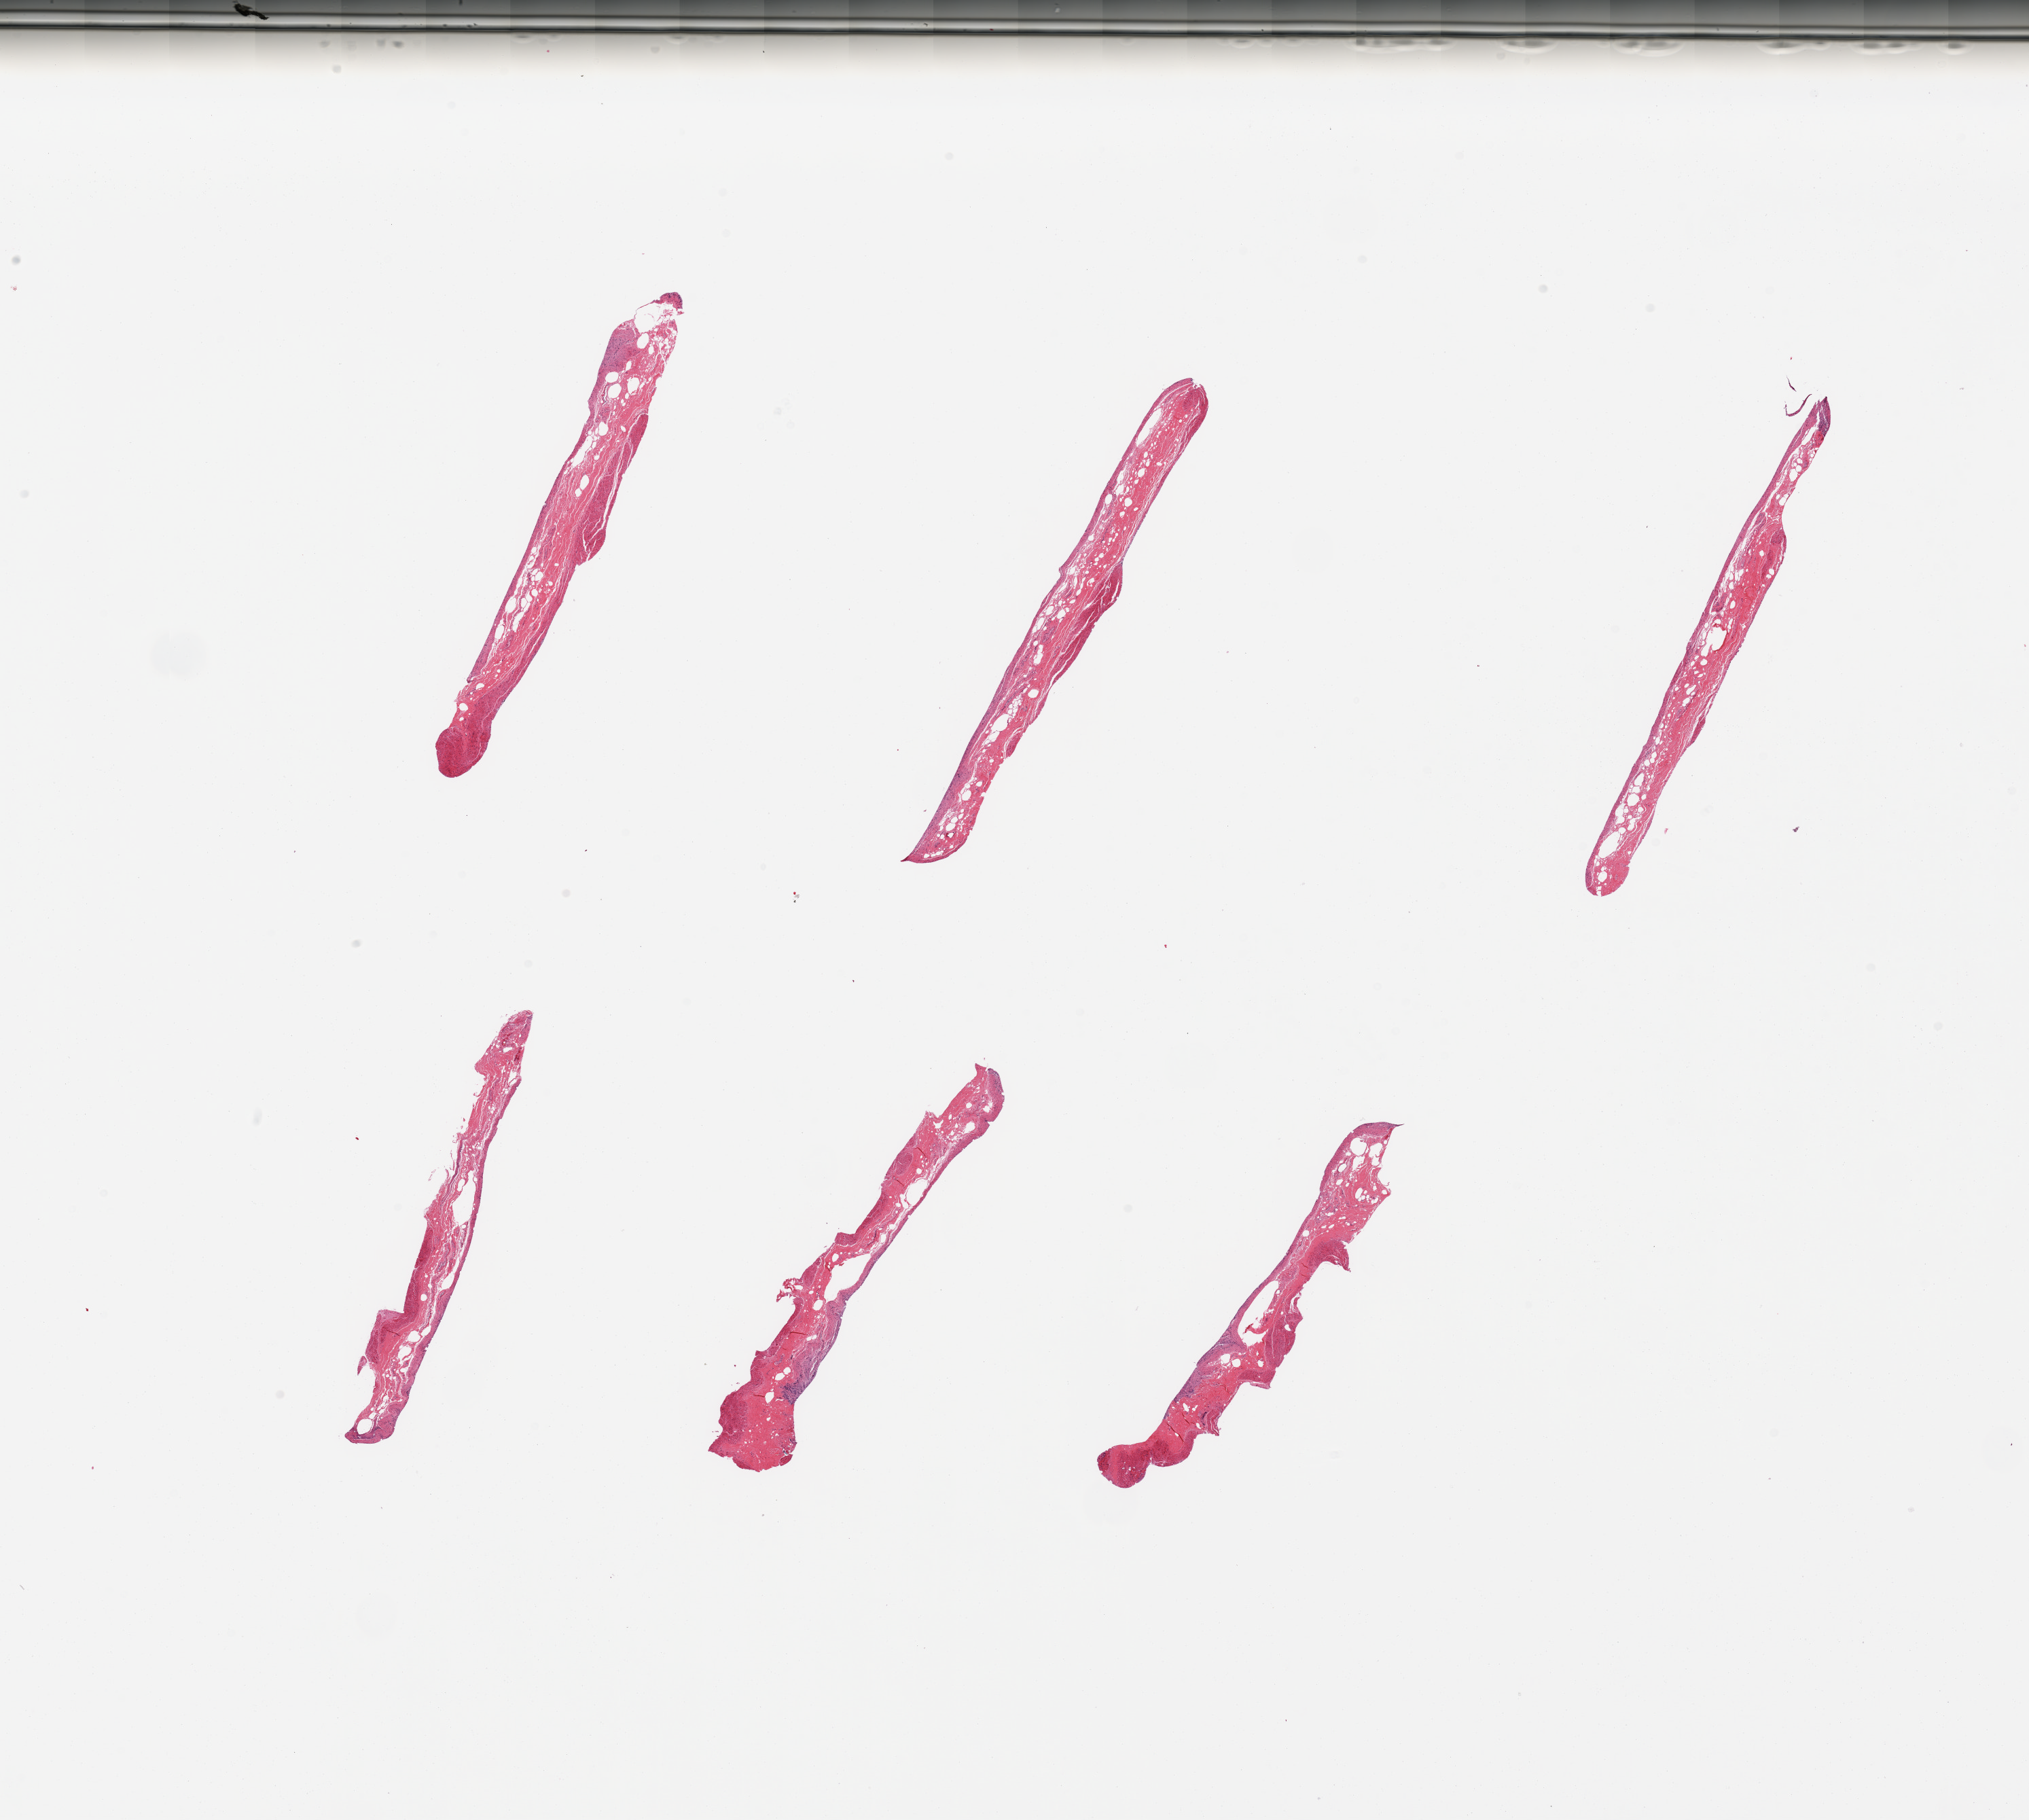
Digitized haematoxylin and eosin-stained section, whole scanned area (about 23.6 x 21.2 mm) shown as a low-resolution overview; PAXgene-fixed paraffin-embedded (PFPE) section; section of stomach (target tissue); tissue donor sample. Donor: male.
Reviewer comment on this tissue sample: 6 pieces; largely submucosa with bits of muscle.